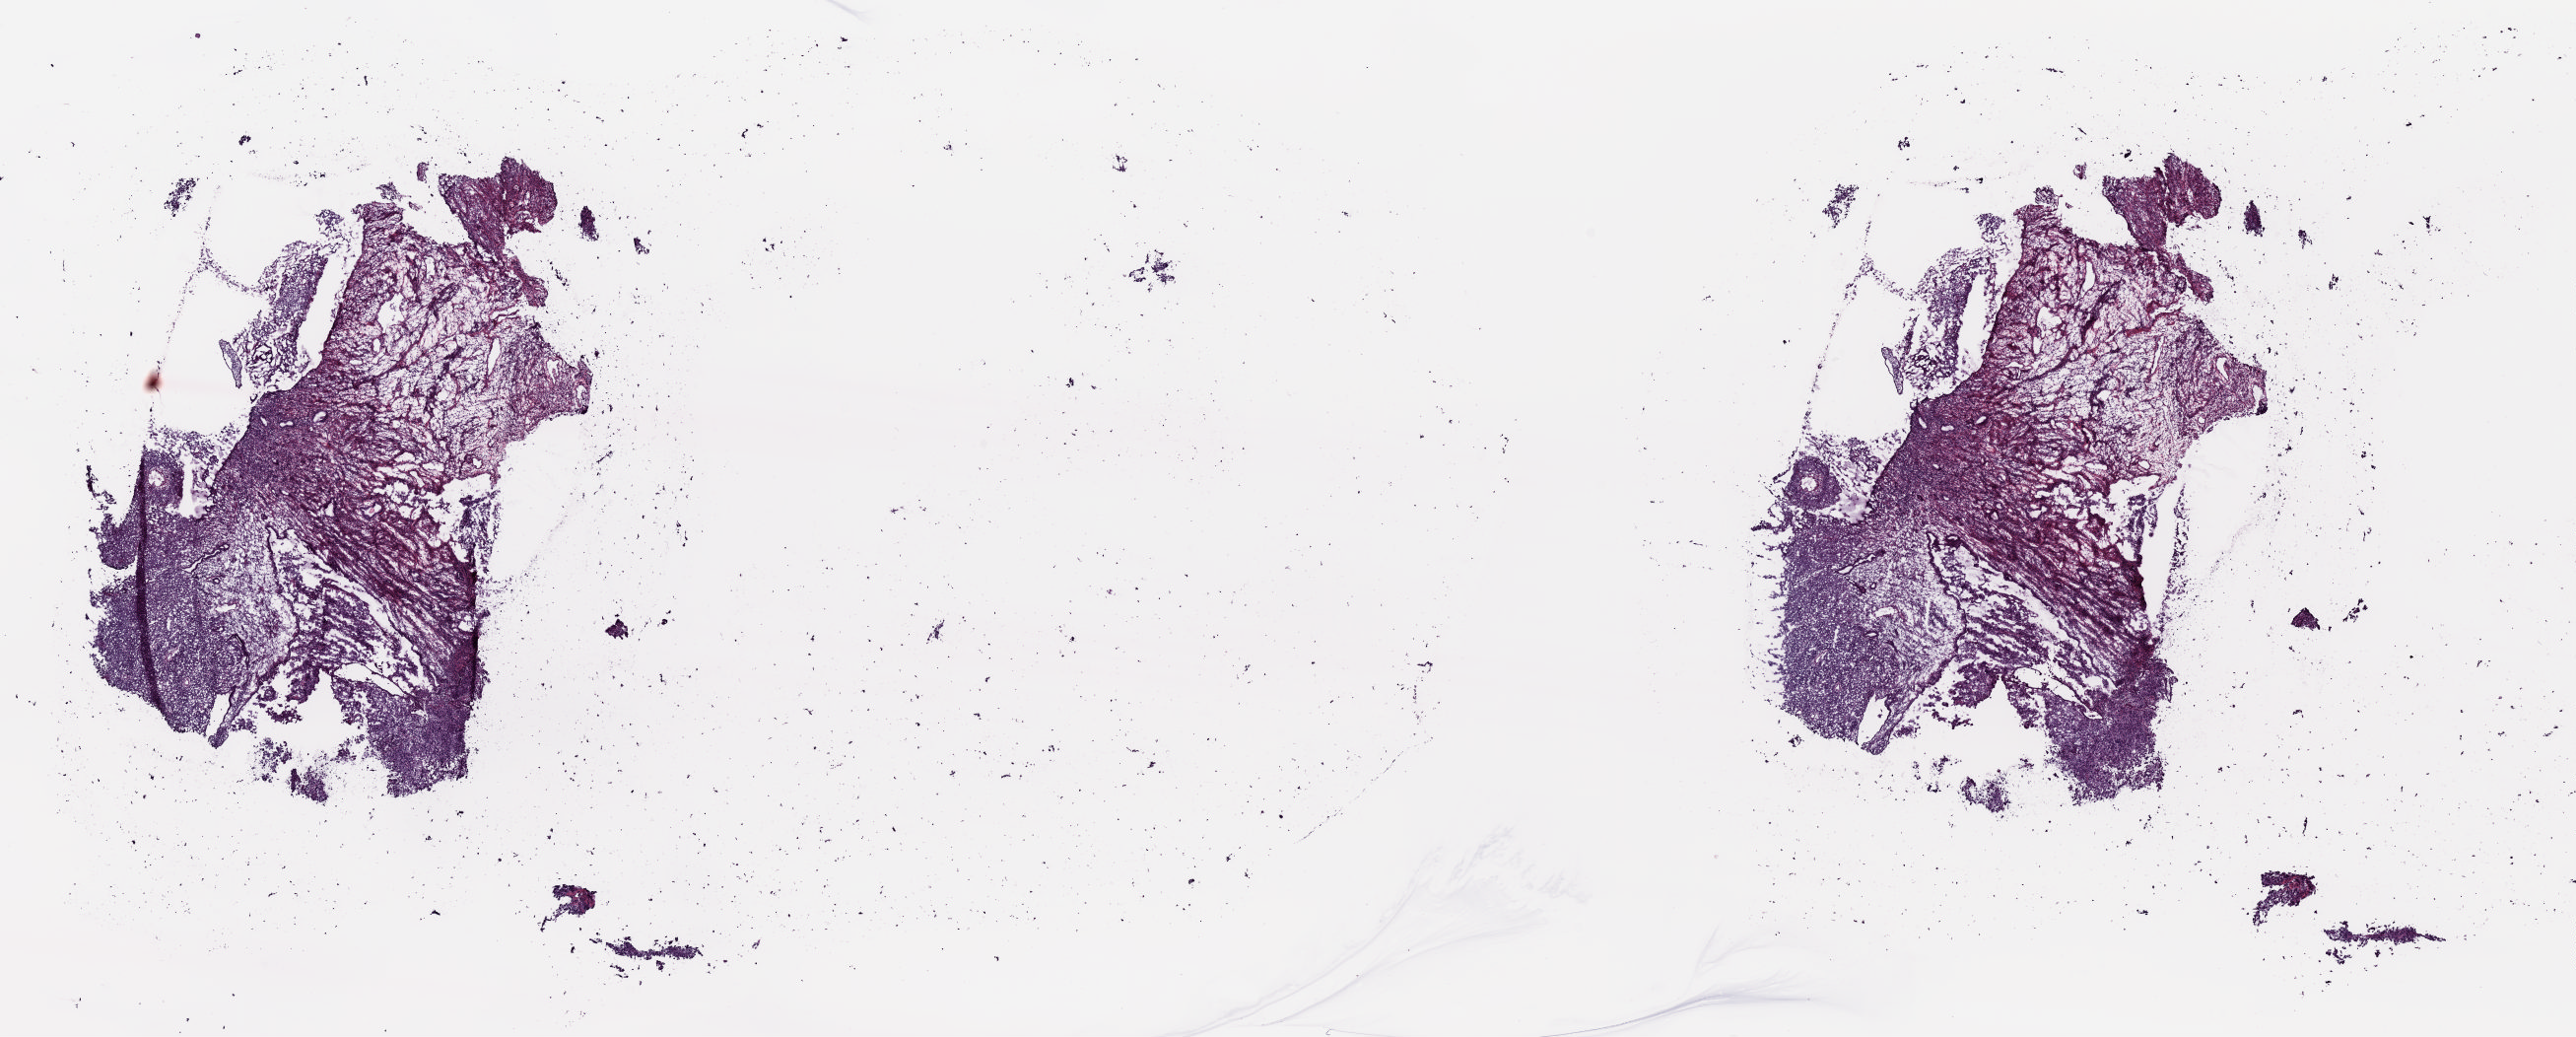
H&E-stained whole-slide image, a low-resolution overview of the entire scanned area, about 20.7 x 8.3 mm. Frozen section from the top of the tissue portion. Solid tissue normal (non-tumour tissue) sample from the uterus. Female patient; age at initial diagnosis 69 years. Composition of this section per pathologist review: tumour cells 0%, tumour nuclei 0%.
This section: solid tissue normal (non-tumour) sample from the same patient. Patient diagnosis: Endometrioid adenocarcinoma, NOS (endometrium).